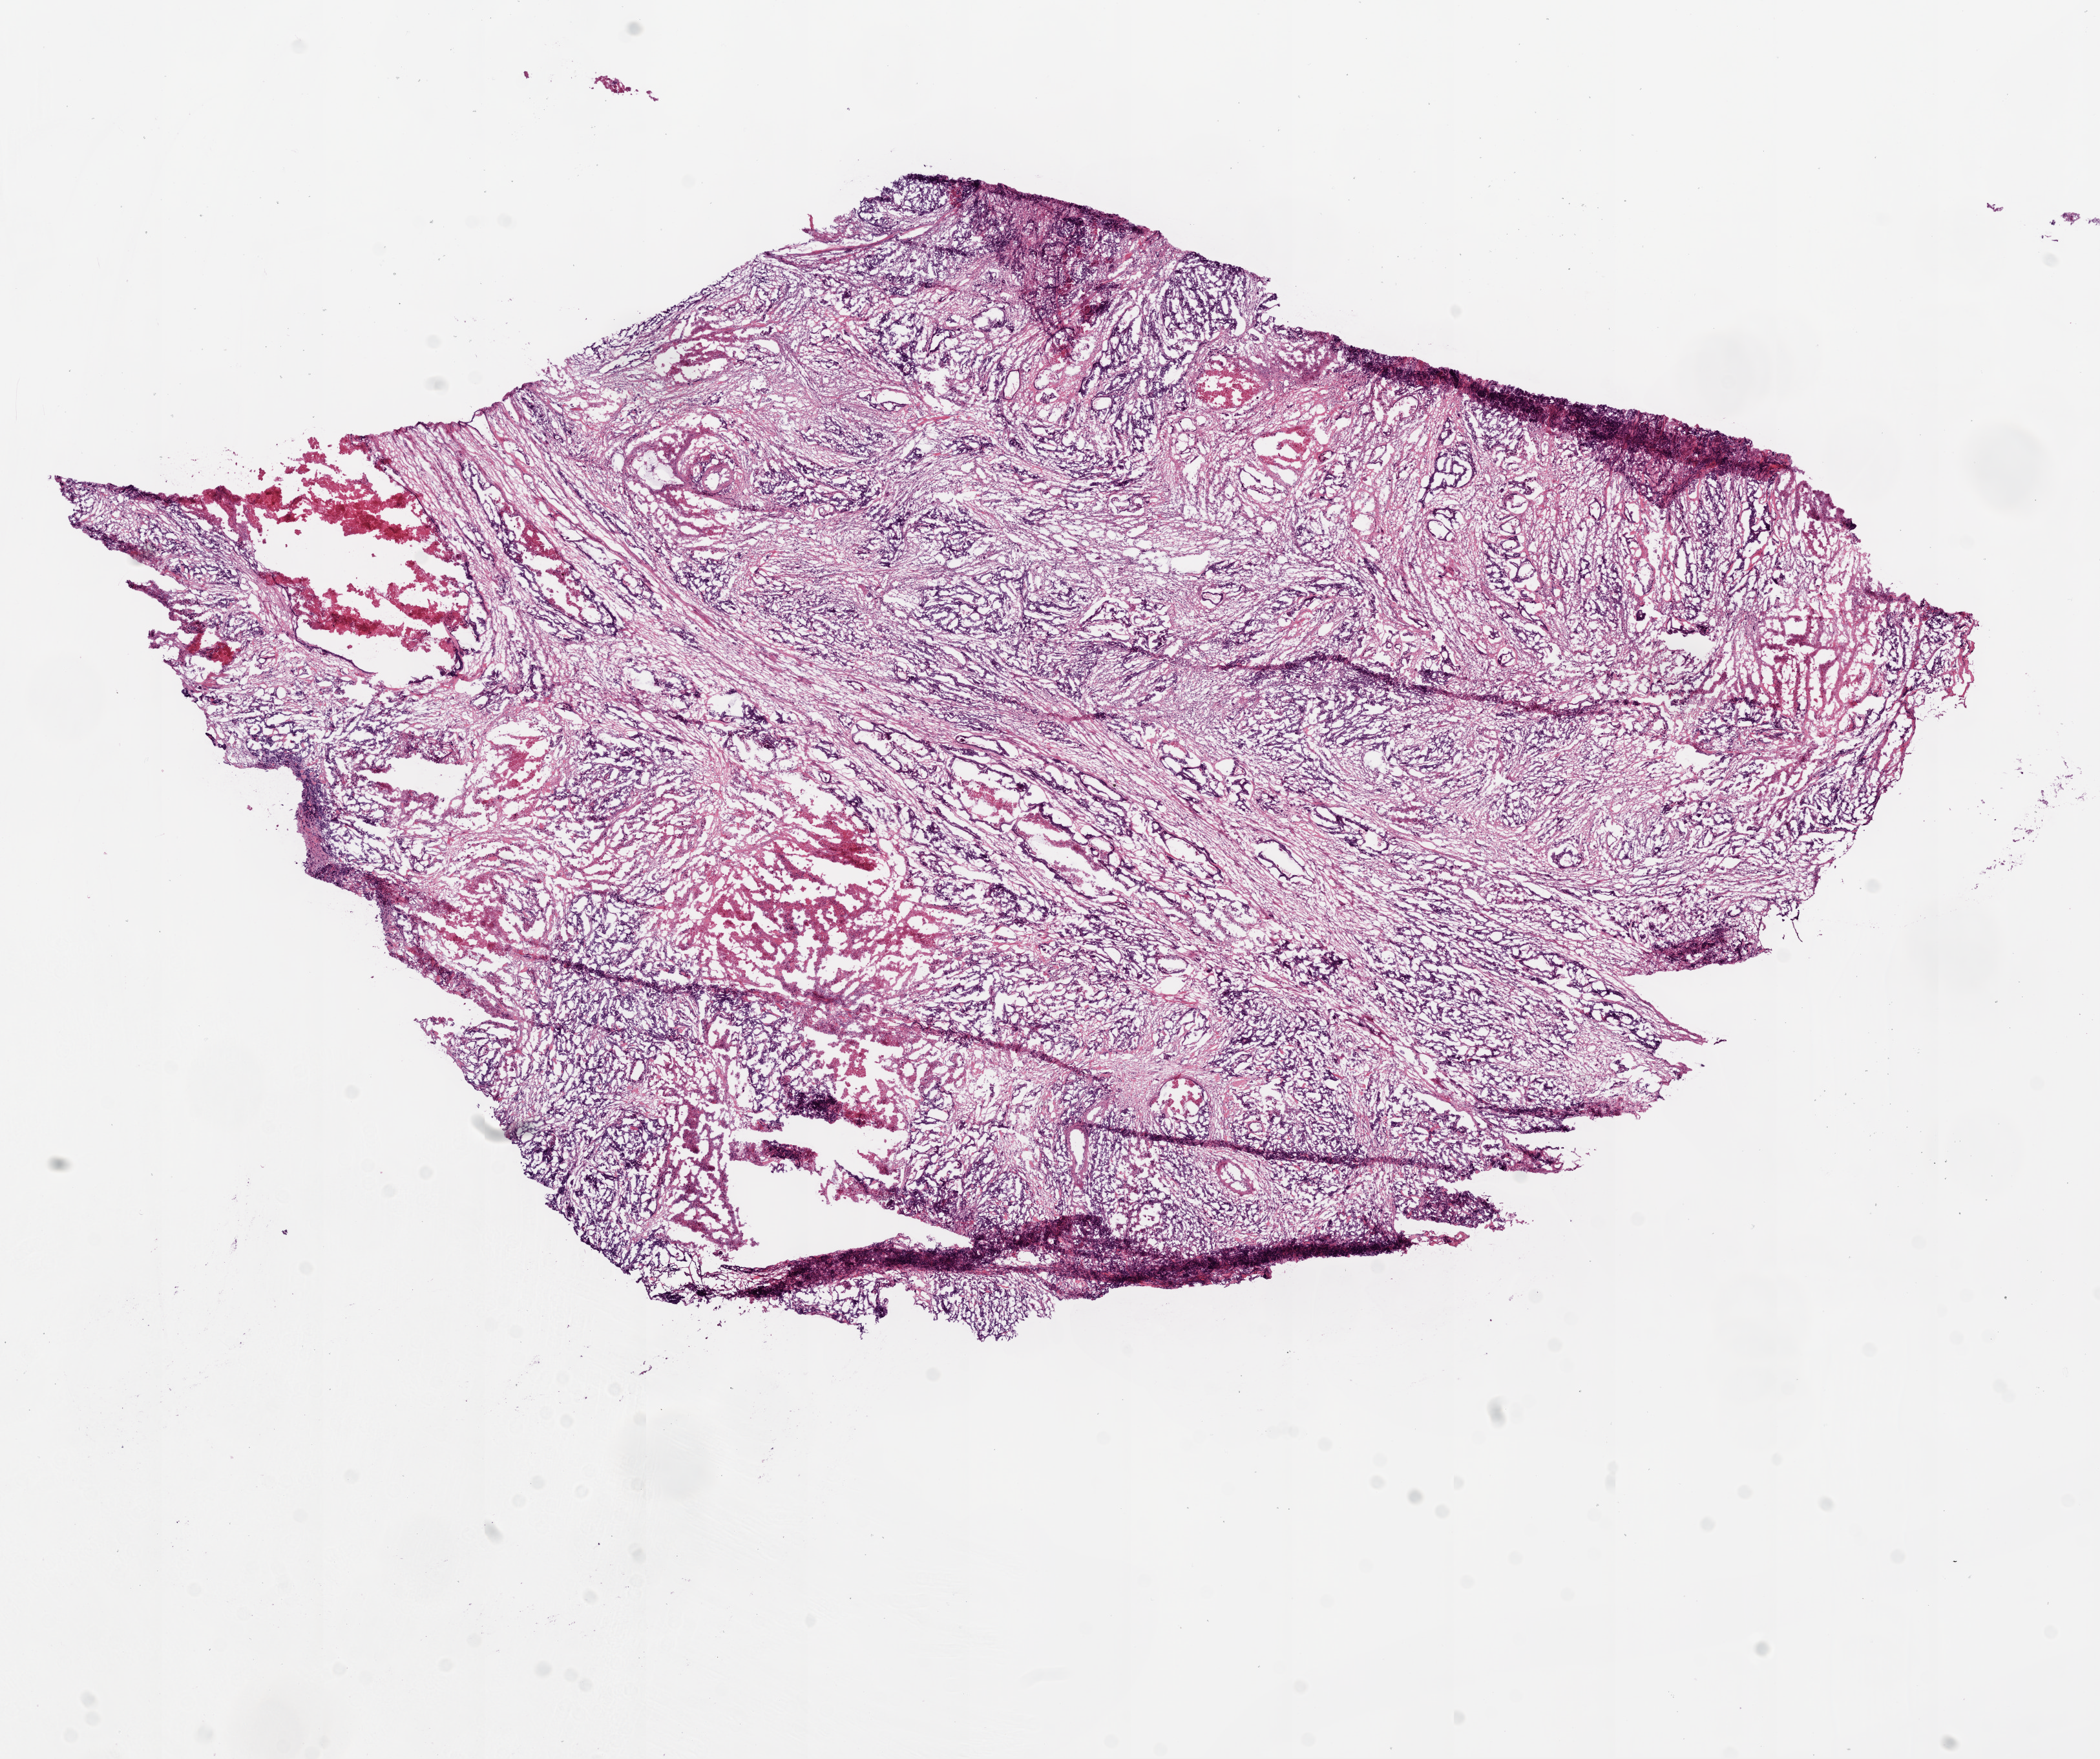
Whole-slide histology image, H&E-stained, whole scanned area (about 13.0 x 10.9 mm, slide scanned at 20x) shown as a low-resolution overview. Frozen section. Colon, primary tumour sample. Female, age 82 years at initial diagnosis. Composition of this section per pathologist review: tumour cells 75%, tumour nuclei 75%, normal cells 0%, stromal cells 10%, necrosis 15%.
AJCC pathologic stage: IV (6th edition). Histologic diagnosis: Adenocarcinoma, NOS (cecum). Lymph nodes positive (case pathology): 13 of 23 examined.